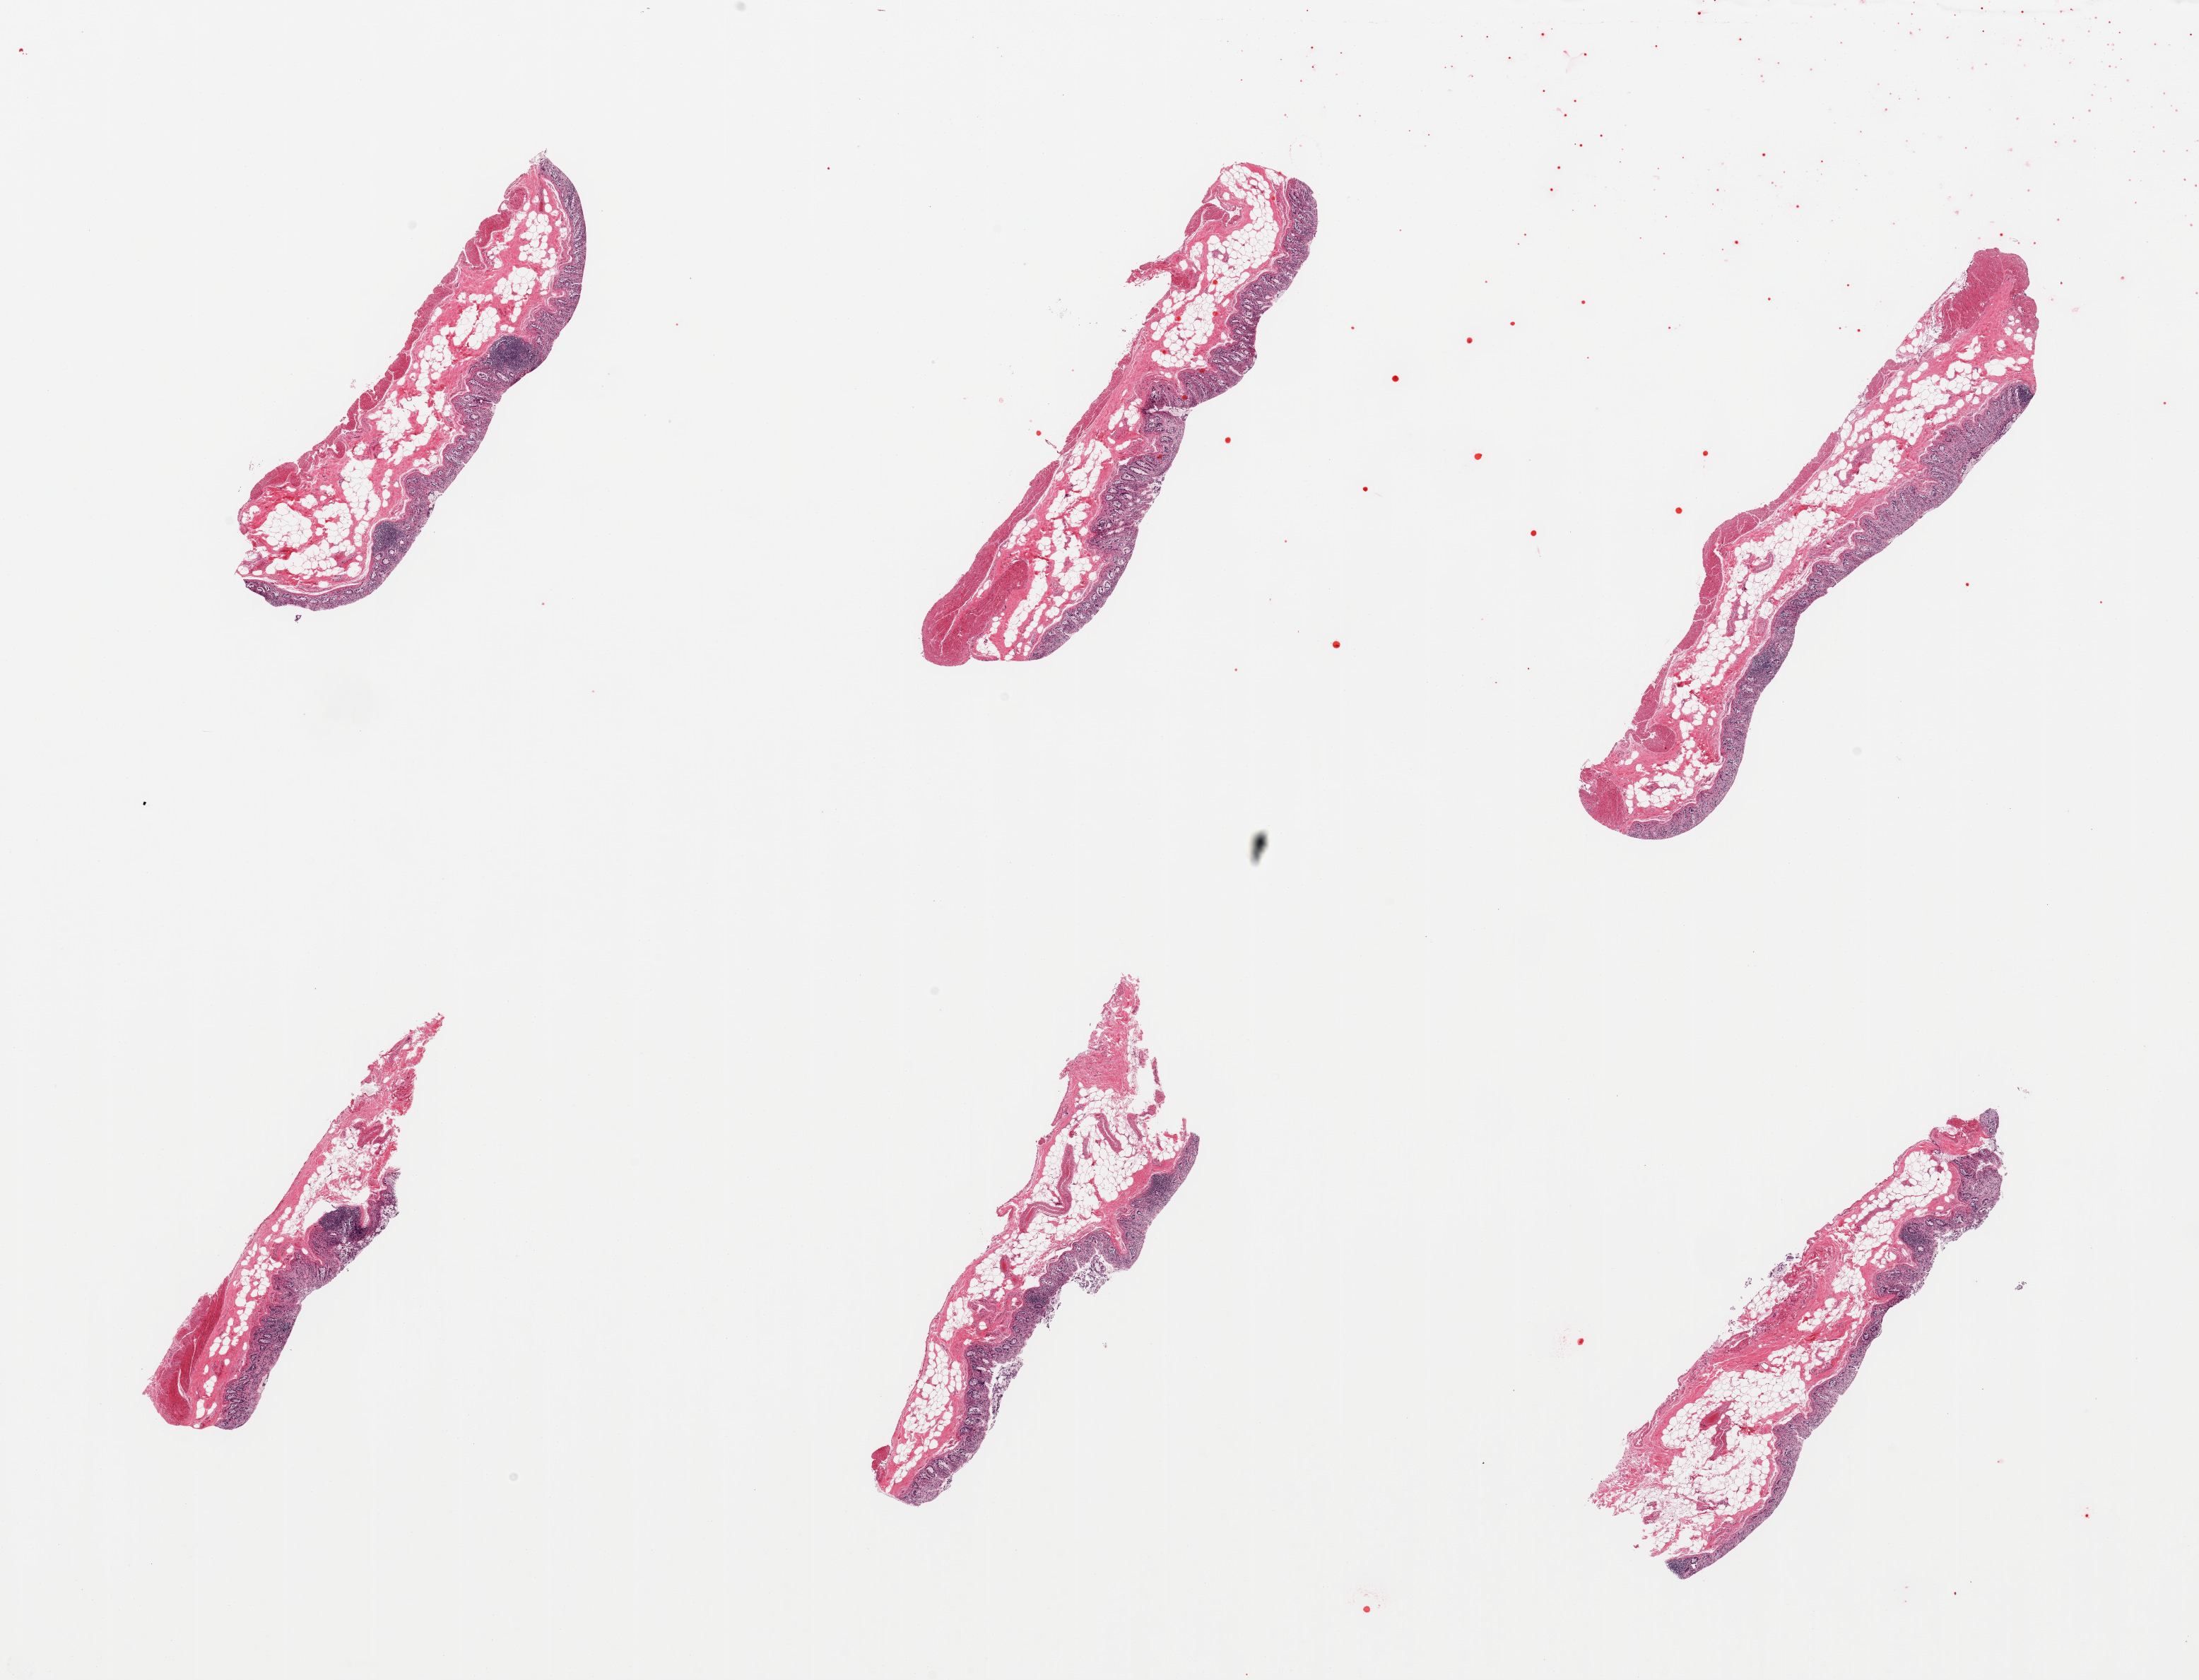
Haematoxylin and eosin whole-slide image — low-resolution overview of the scanned area, about 24.6 x 18.8 mm (from a 20x scan), PAXgene-fixed, paraffin-embedded tissue, sampled site (target tissue): transverse colon, tissue donor sample. Donor: male.
• pathologist's review note for this sample: 6 pieces, mucosa up to ~0.5mm, 30-40% thickness, autolysis moderately advanced, apporaching score '3' in areas